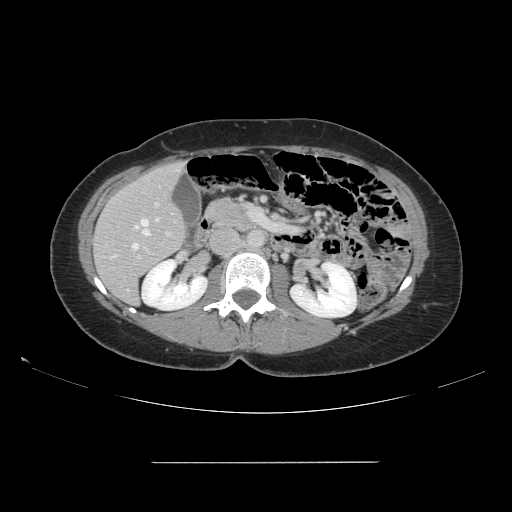
Contrast-enhanced abdominal CT, one axial slice. Slice 69 of 151 in the series (ordered by position). Soft-tissue window (W 400 / L 40 HU). 512 × 512 image matrix, field of view 421 × 421 mm. Female patient, age 46 years. Case-level facts recorded for this patient, not image findings: diagnosis: colorectal cancer liver metastases, imaged before liver resection; multiple liver metastases: yes; largest metastasis: 3 cm; disease in both lobes: yes.
Outlined on this slice (outlined manually by an expert reader):
- hepatic veins: bounding box [x1, y1, x2, y2] px = [132, 218, 159, 250]
- liver: [94, 163, 186, 304]
- planned liver remnant (the part of the liver to remain after resection): [94, 163, 186, 304]
- portal vein (with intrahepatic branches): [137, 202, 171, 259]